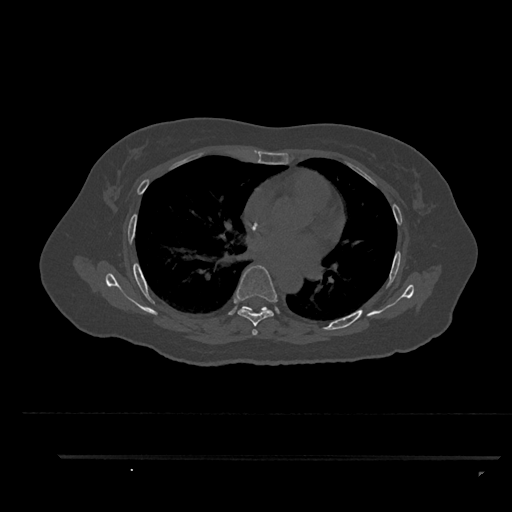
CT including the spine, one axial slice. Position 549 of 797 along the scan axis. Bone window (W 1800 / L 400 HU). 0.5 mm slice thickness. 512 × 512 image matrix, field of view 408 × 408 mm. Patient: female, 44 years. From the clinical record (not read from this slice): primary cancer: renal.
Outlined on this slice (semi-automatically segmented with operator editing):
- T6 vertebra: bounding box <236,265,277,335> (left, top, right, bottom; pixels)
- T7 vertebra: <242,306,267,313>